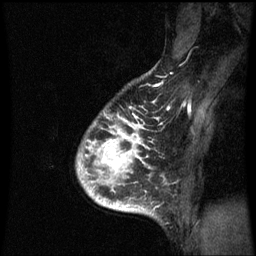
Breast MRI (dynamic contrast-enhanced), one sagittal slice. Position 52 of 60 along the scan axis. Dynamic contrast-enhanced series, image 2 of 3 at this slice position (ordered by acquisition). 1.5 T. TE 4.2 ms, TR 8.9 ms. 2 mm slice thickness. 256 × 256 image matrix. Female patient, age 35 years. From the clinical record (not read from this slice): setting: breast cancer imaged before/during neoadjuvant chemotherapy; receptor status: HR-positive, HER2-negative.
Outlined on this slice (semi-automatic segmentation, software-assisted and operator-edited):
- analysis volume of interest (the breast-tissue region the enhancement analysis was run in; not a lesion): box from (x=79, y=102) to (x=162, y=215) px
- tumour enhancement mask (voxels above the 70 % enhancement threshold inside the analysis volume of interest): (x=79, y=116)–(x=150, y=211)